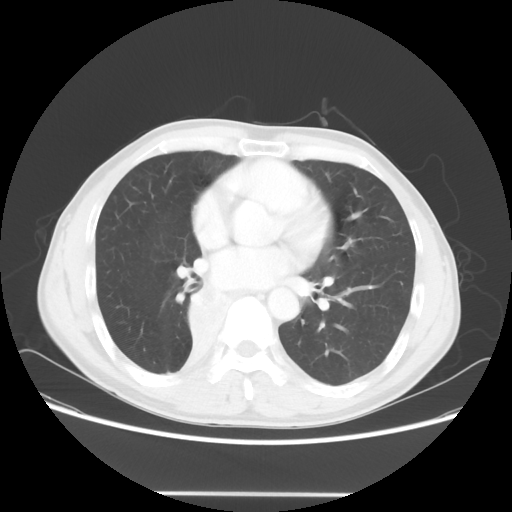
Chest CT, one axial slice. Slice 29 of 62 in the series (ordered by position). 120 kVp. Lung window (W 1500 / L -600 HU). 512 × 512 image matrix. Patient: male, 47 years. Case-level facts recorded for this patient, not image findings: clinical TNM (as recorded): T2 N0 M0; histopathological grade: G2.
Annotated regions visible in this slice (bounding box drawn by a radiologist):
- lung tumour (recorded histology: squamous cell carcinoma): bounding box <180,283,242,344> (left, top, right, bottom; pixels)